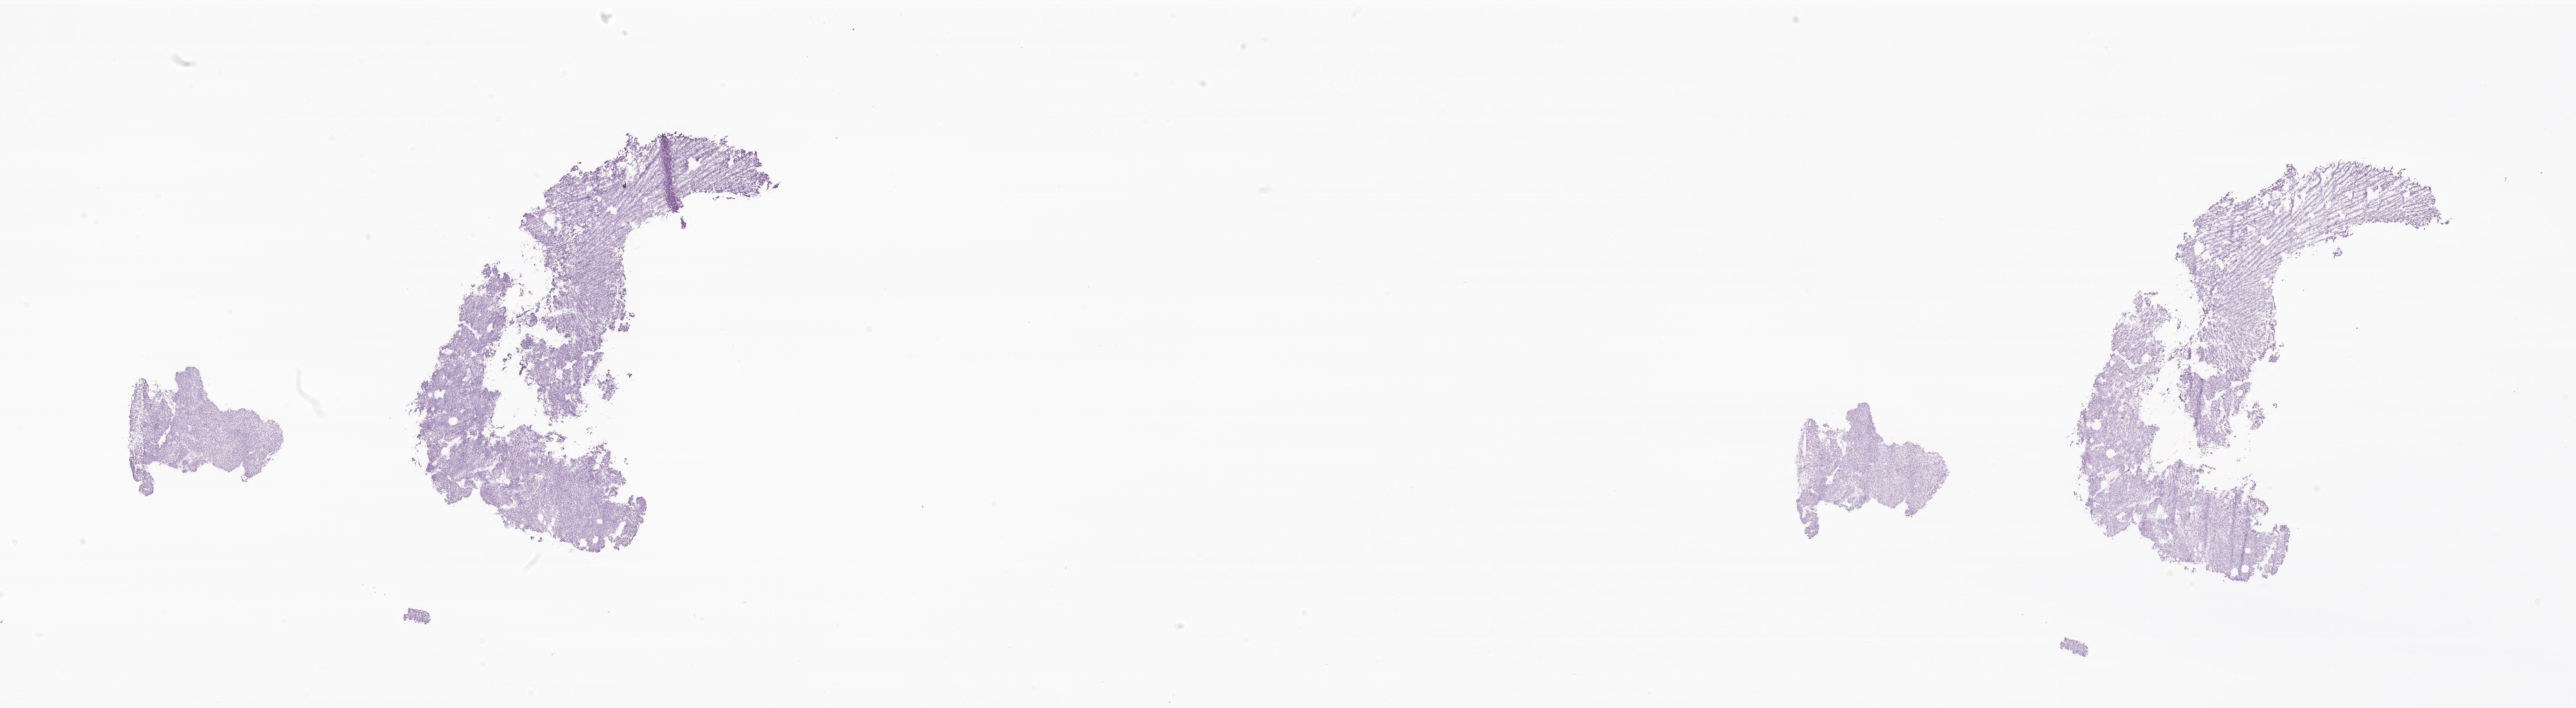
Digitized hematoxylin and eosin (H&E)-stained section of tumor tissue from the soft tissues of head and neck — low-resolution overview of the scanned area, about 37.1 x 10.2 mm, frozen section (OCT-embedded). Patient female; age 131 months (10 years 11 months).
Recorded diagnosis: Synovial sarcoma, biphasic. Tissue or organ of origin (case record): connective, subcutaneous and other soft tissues of head, face, and neck.